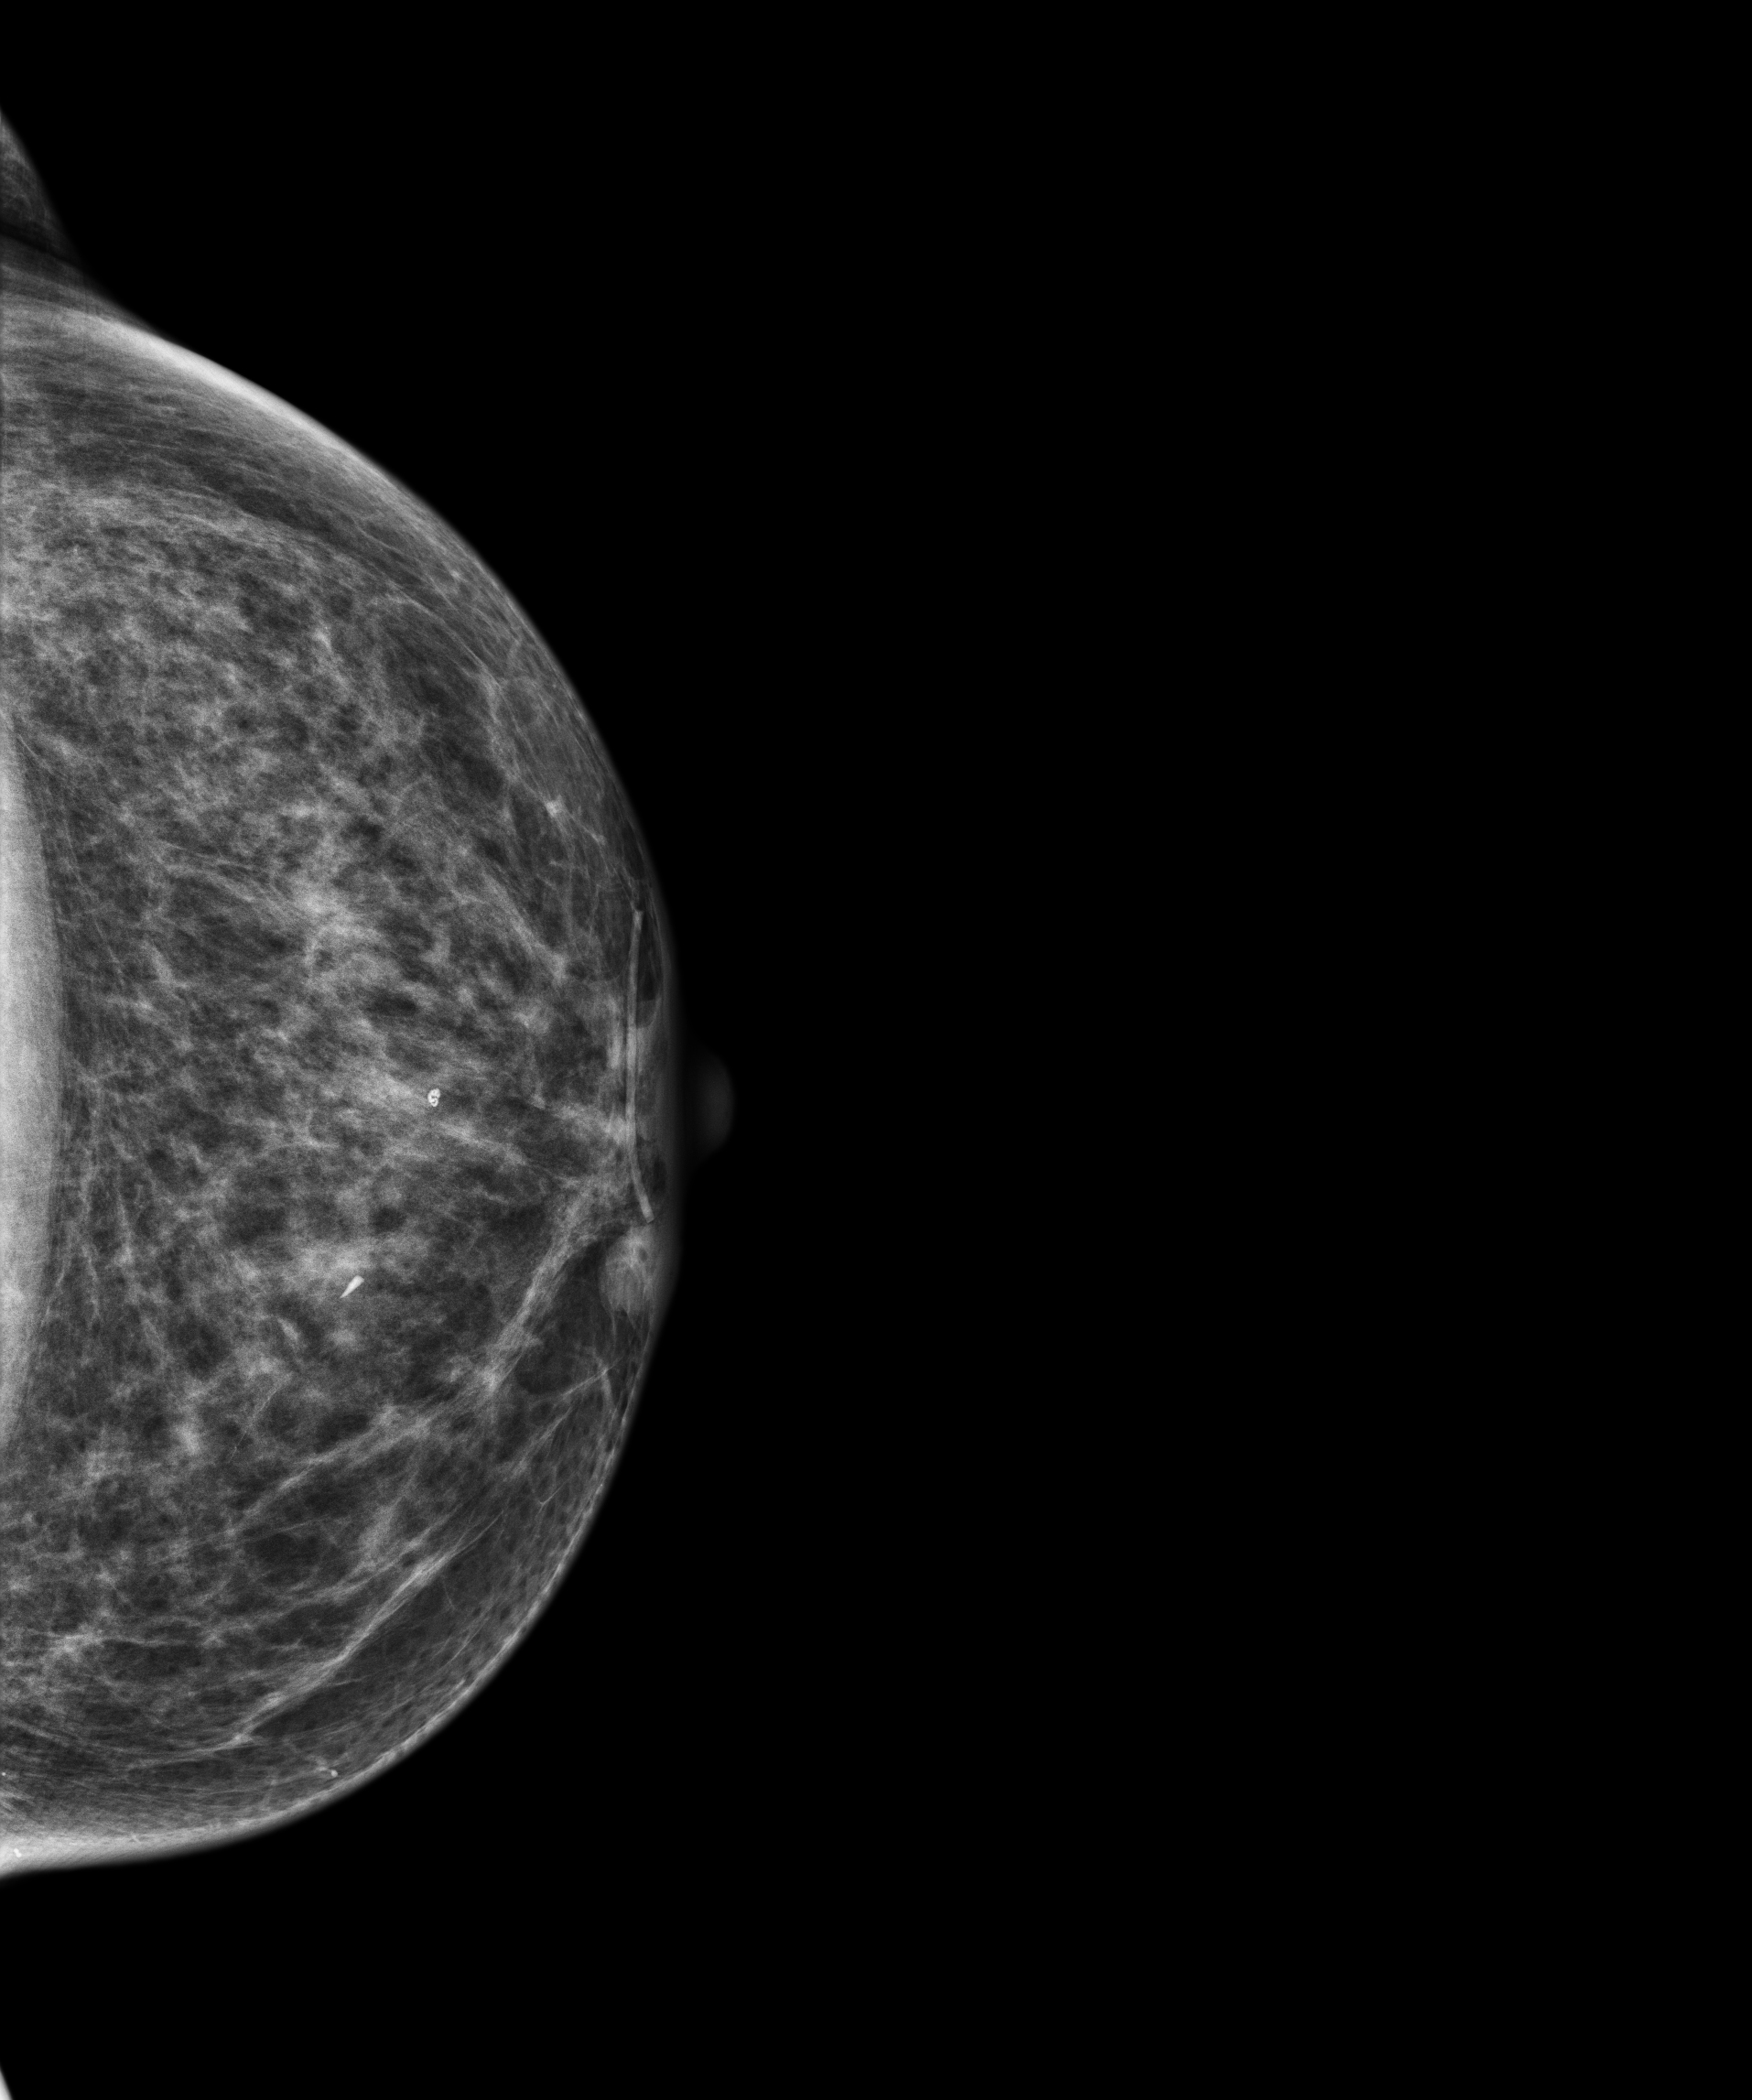
Annual screening mammography examination; system: Senographe Essential ADS_56.21.3. Patient aged 70 years (female).
Image type: full-field digital mammogram. Breast: left. Projection: cranio-caudal projection.